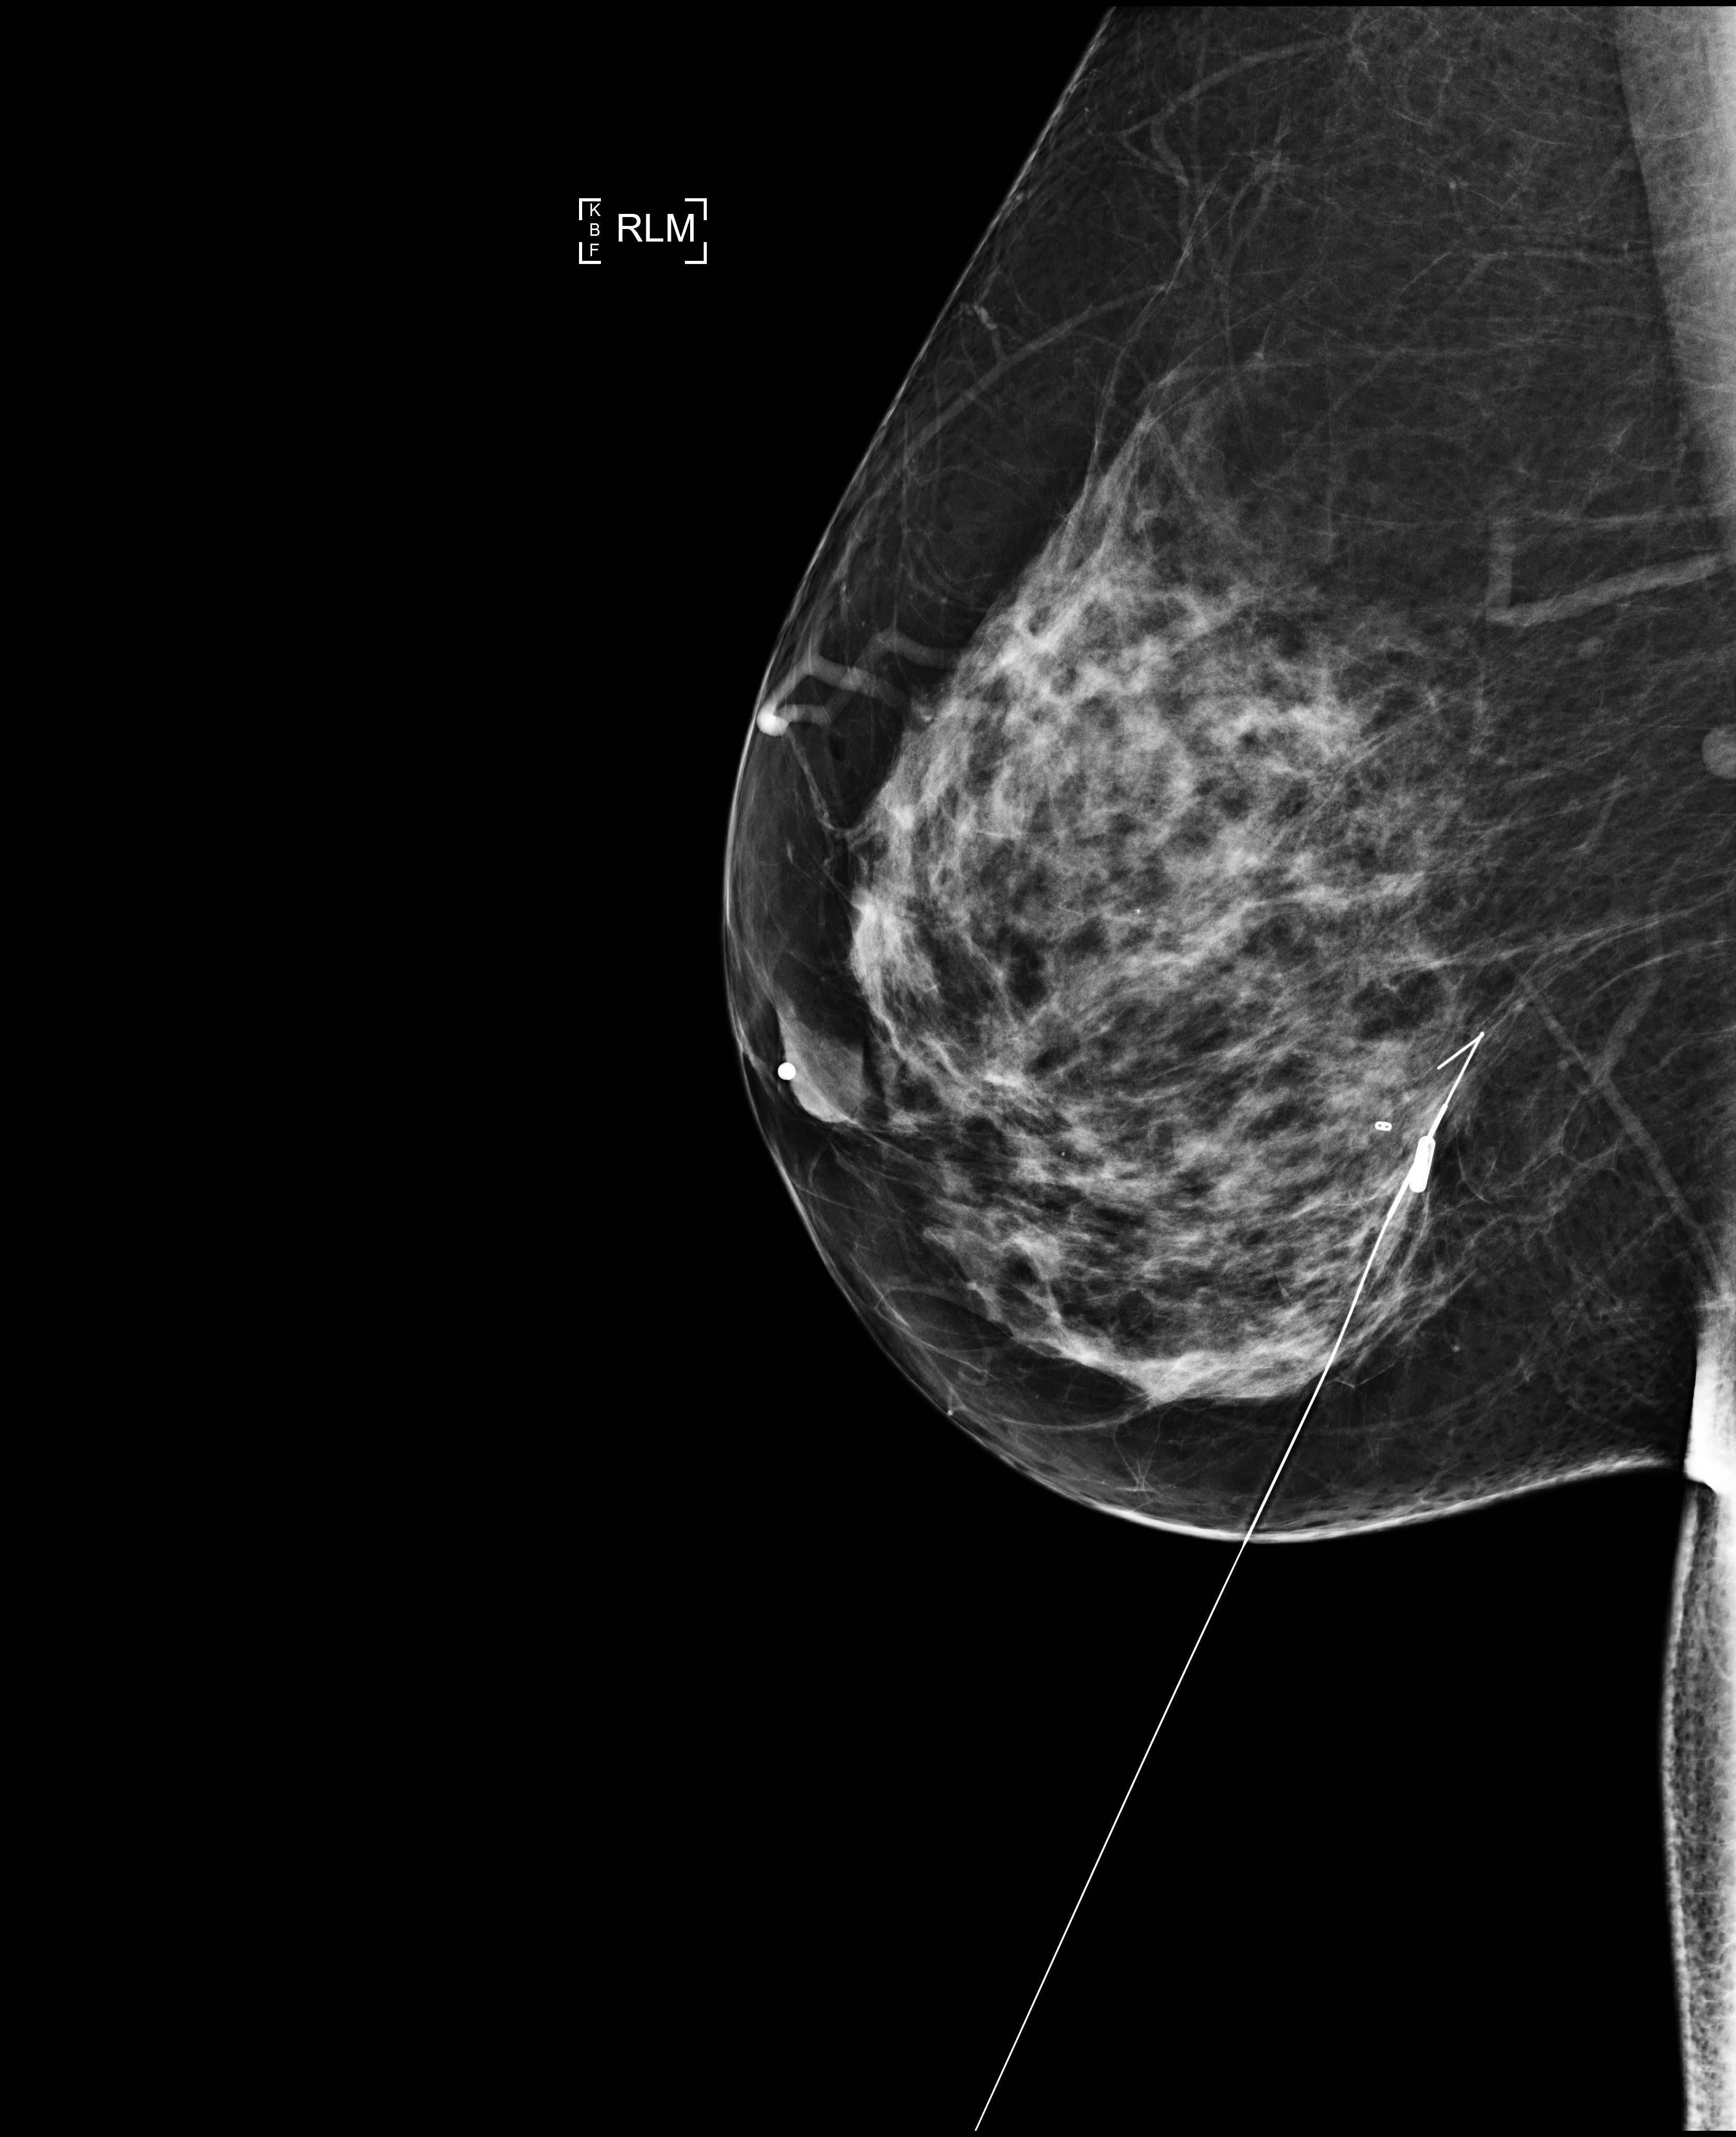
Diagnostic examination (additional views); system: Selenia Dimensions. Female patient, age 50 years.
Image type: full-field digital mammogram. Breast: right. Projection: LM view.